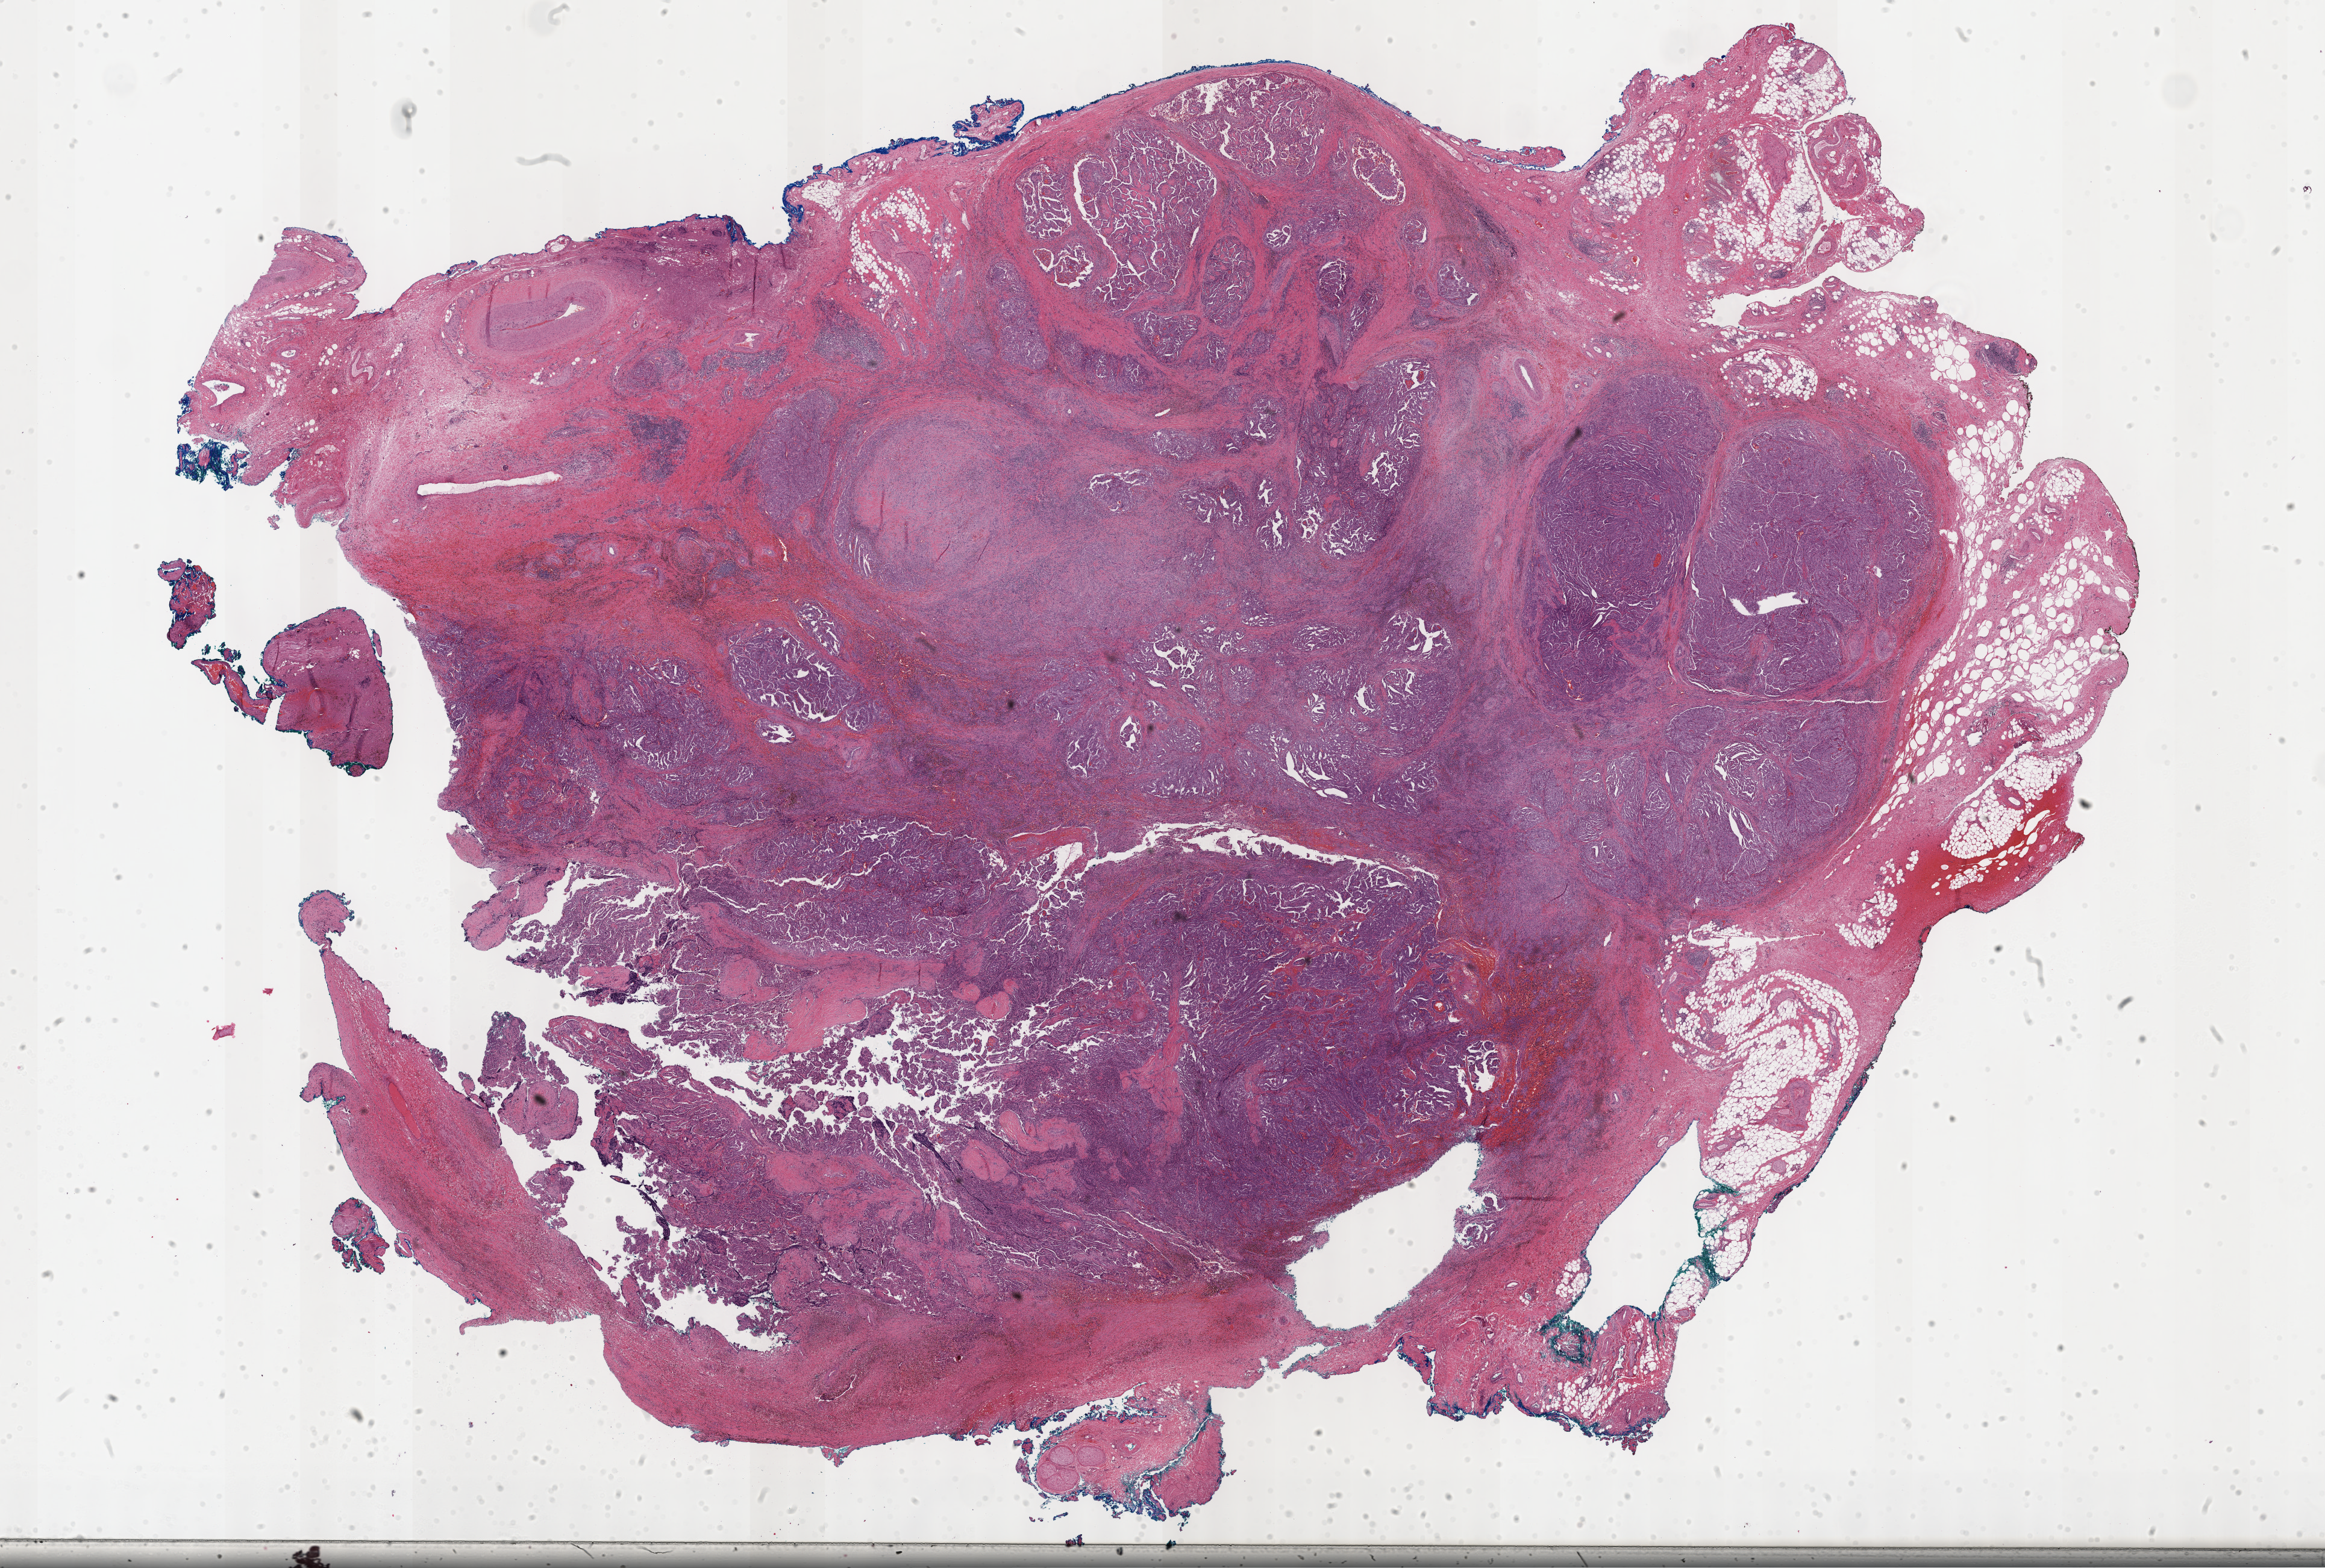
Digitized H&E tissue section (whole slide) — whole scanned area (about 31.2 x 21.1 mm) shown as a low-resolution overview; formalin-fixed paraffin-embedded (FFPE) diagnostic section; primary tumour sample from the thyroid. Female, age 74 years at initial diagnosis.
AJCC pathologic stage: IVA. Laterality: right. Histologic diagnosis: Papillary carcinoma, NOS (thyroid gland).